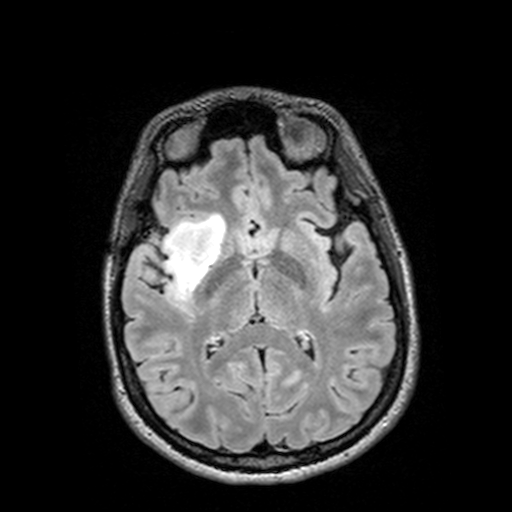
Brain MRI from a brain-tumour surgery series, one axial slice. Slice 71 of 144 in the series (ordered by position). T2 FLAIR. 512 × 512 image matrix, field of view 250 × 250 mm. From the clinical record (not read from this slice): histopathology: Astrocytoma; WHO grade: 3; IDH mutation: yes; tumour location: Right Insular Temporal.
Structures marked on this image (manually delineated by an expert):
- tumour: bounding box [x1, y1, x2, y2] px = [126, 213, 232, 298]